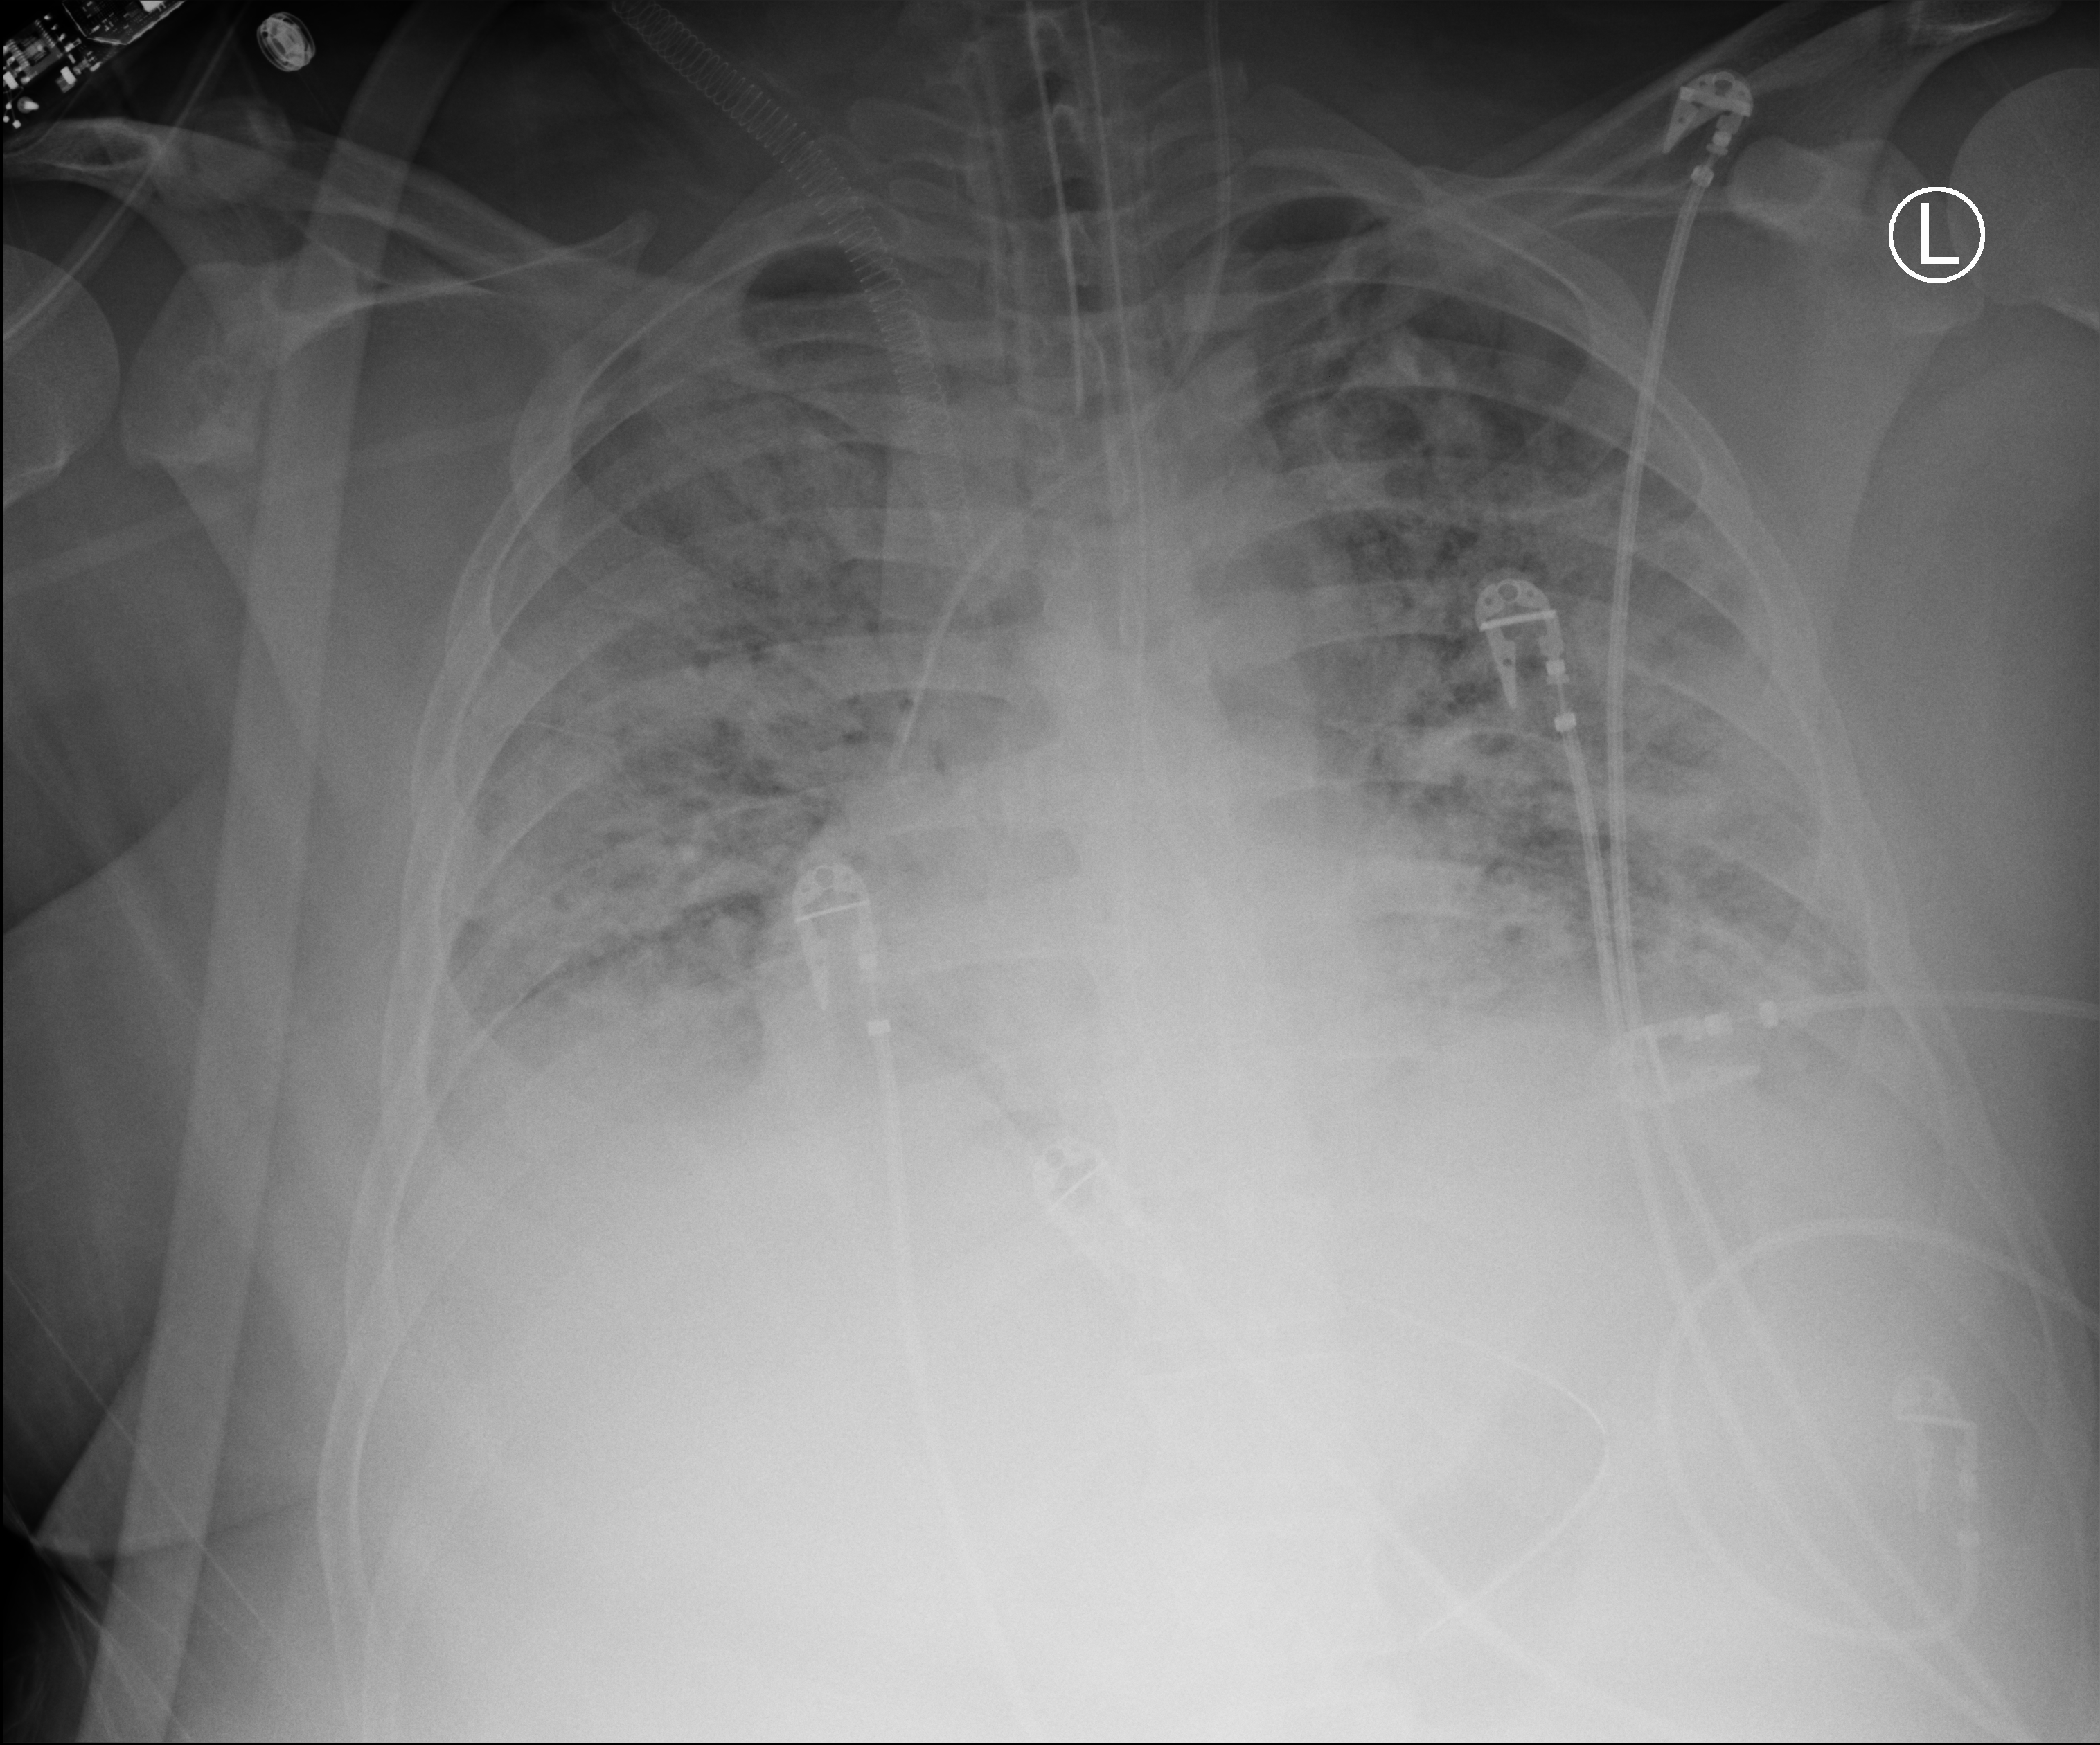
Bedside chest radiograph (computed radiography). Adult patient hospitalised with COVID-19, age 18–59 years.
Admission-level facts for this patient (not findings on this image; timing relative to this image not recorded): other chronic lung disease (admission record): no.